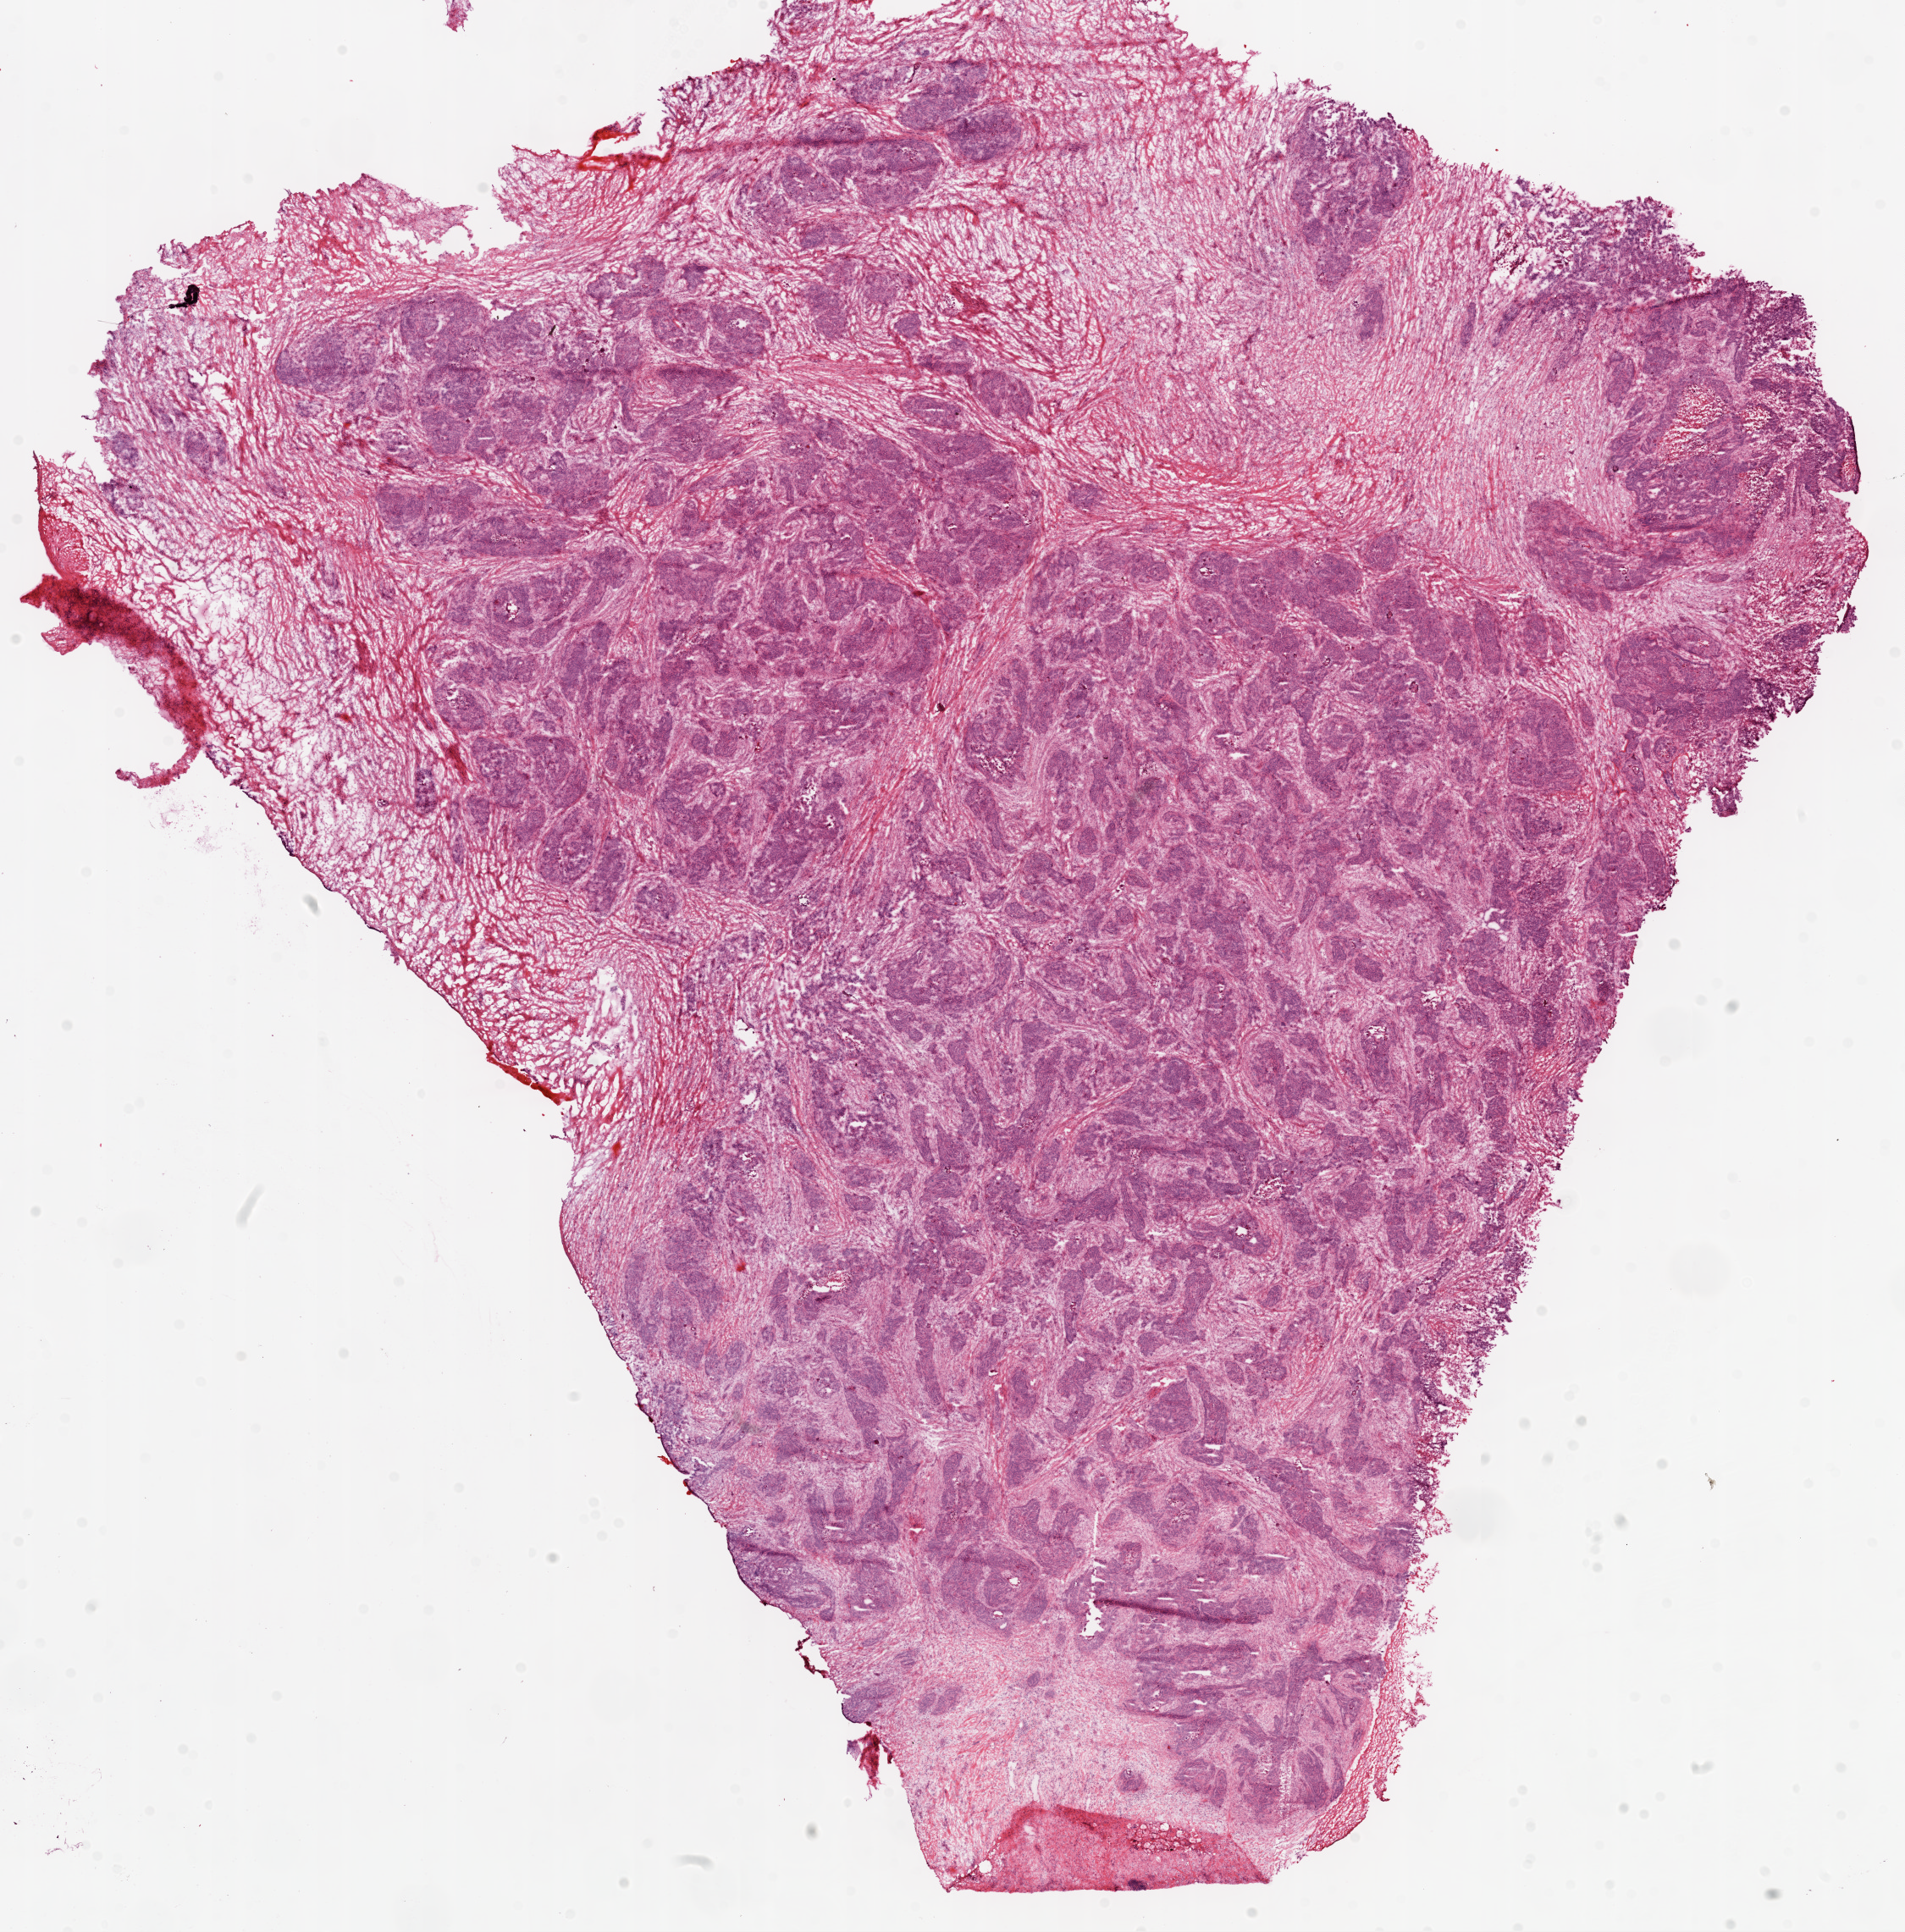
Hematoxylin and eosin (H&E) stained whole-slide image — whole scanned area (about 18.1 x 18.3 mm, from a 20x scan) shown as a low-resolution overview, frozen section from the top of the tissue portion, primary tumour sample from the ovary. Female, age 71 years at initial diagnosis. Histologic grade: G3 (poorly differentiated). Composition of this section per pathologist review: tumour cells 60%, tumour nuclei 65%, normal cells 0%, stromal cells 35%, necrosis 5%.
Diagnosis: Serous cystadenocarcinoma, NOS. FIGO stage: IIIC.